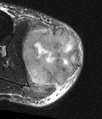
MRI of an extremity soft-tissue mass, one axial slice; position 28 of 48 along the scan axis; T2-weighted fat-saturated; MR volume resampled by the dataset authors to the PET/CT grid (not the native acquisition matrix); 102 × 119 image matrix, field of view 100 × 116 mm. Male patient. Case-level facts recorded for this patient, not image findings: histological type: pleiomorphic liposarcoma; grade: high; site of the primary tumour: right calf.
Structures marked on this image (expert contour drawn on MRI and transferred to this co-registered scan by the dataset authors):
- gross tumour volume including surrounding oedema: bounding box [x1, y1, x2, y2] px = [21, 28, 79, 91]
- gross tumour volume (mass): [21, 28, 79, 88]